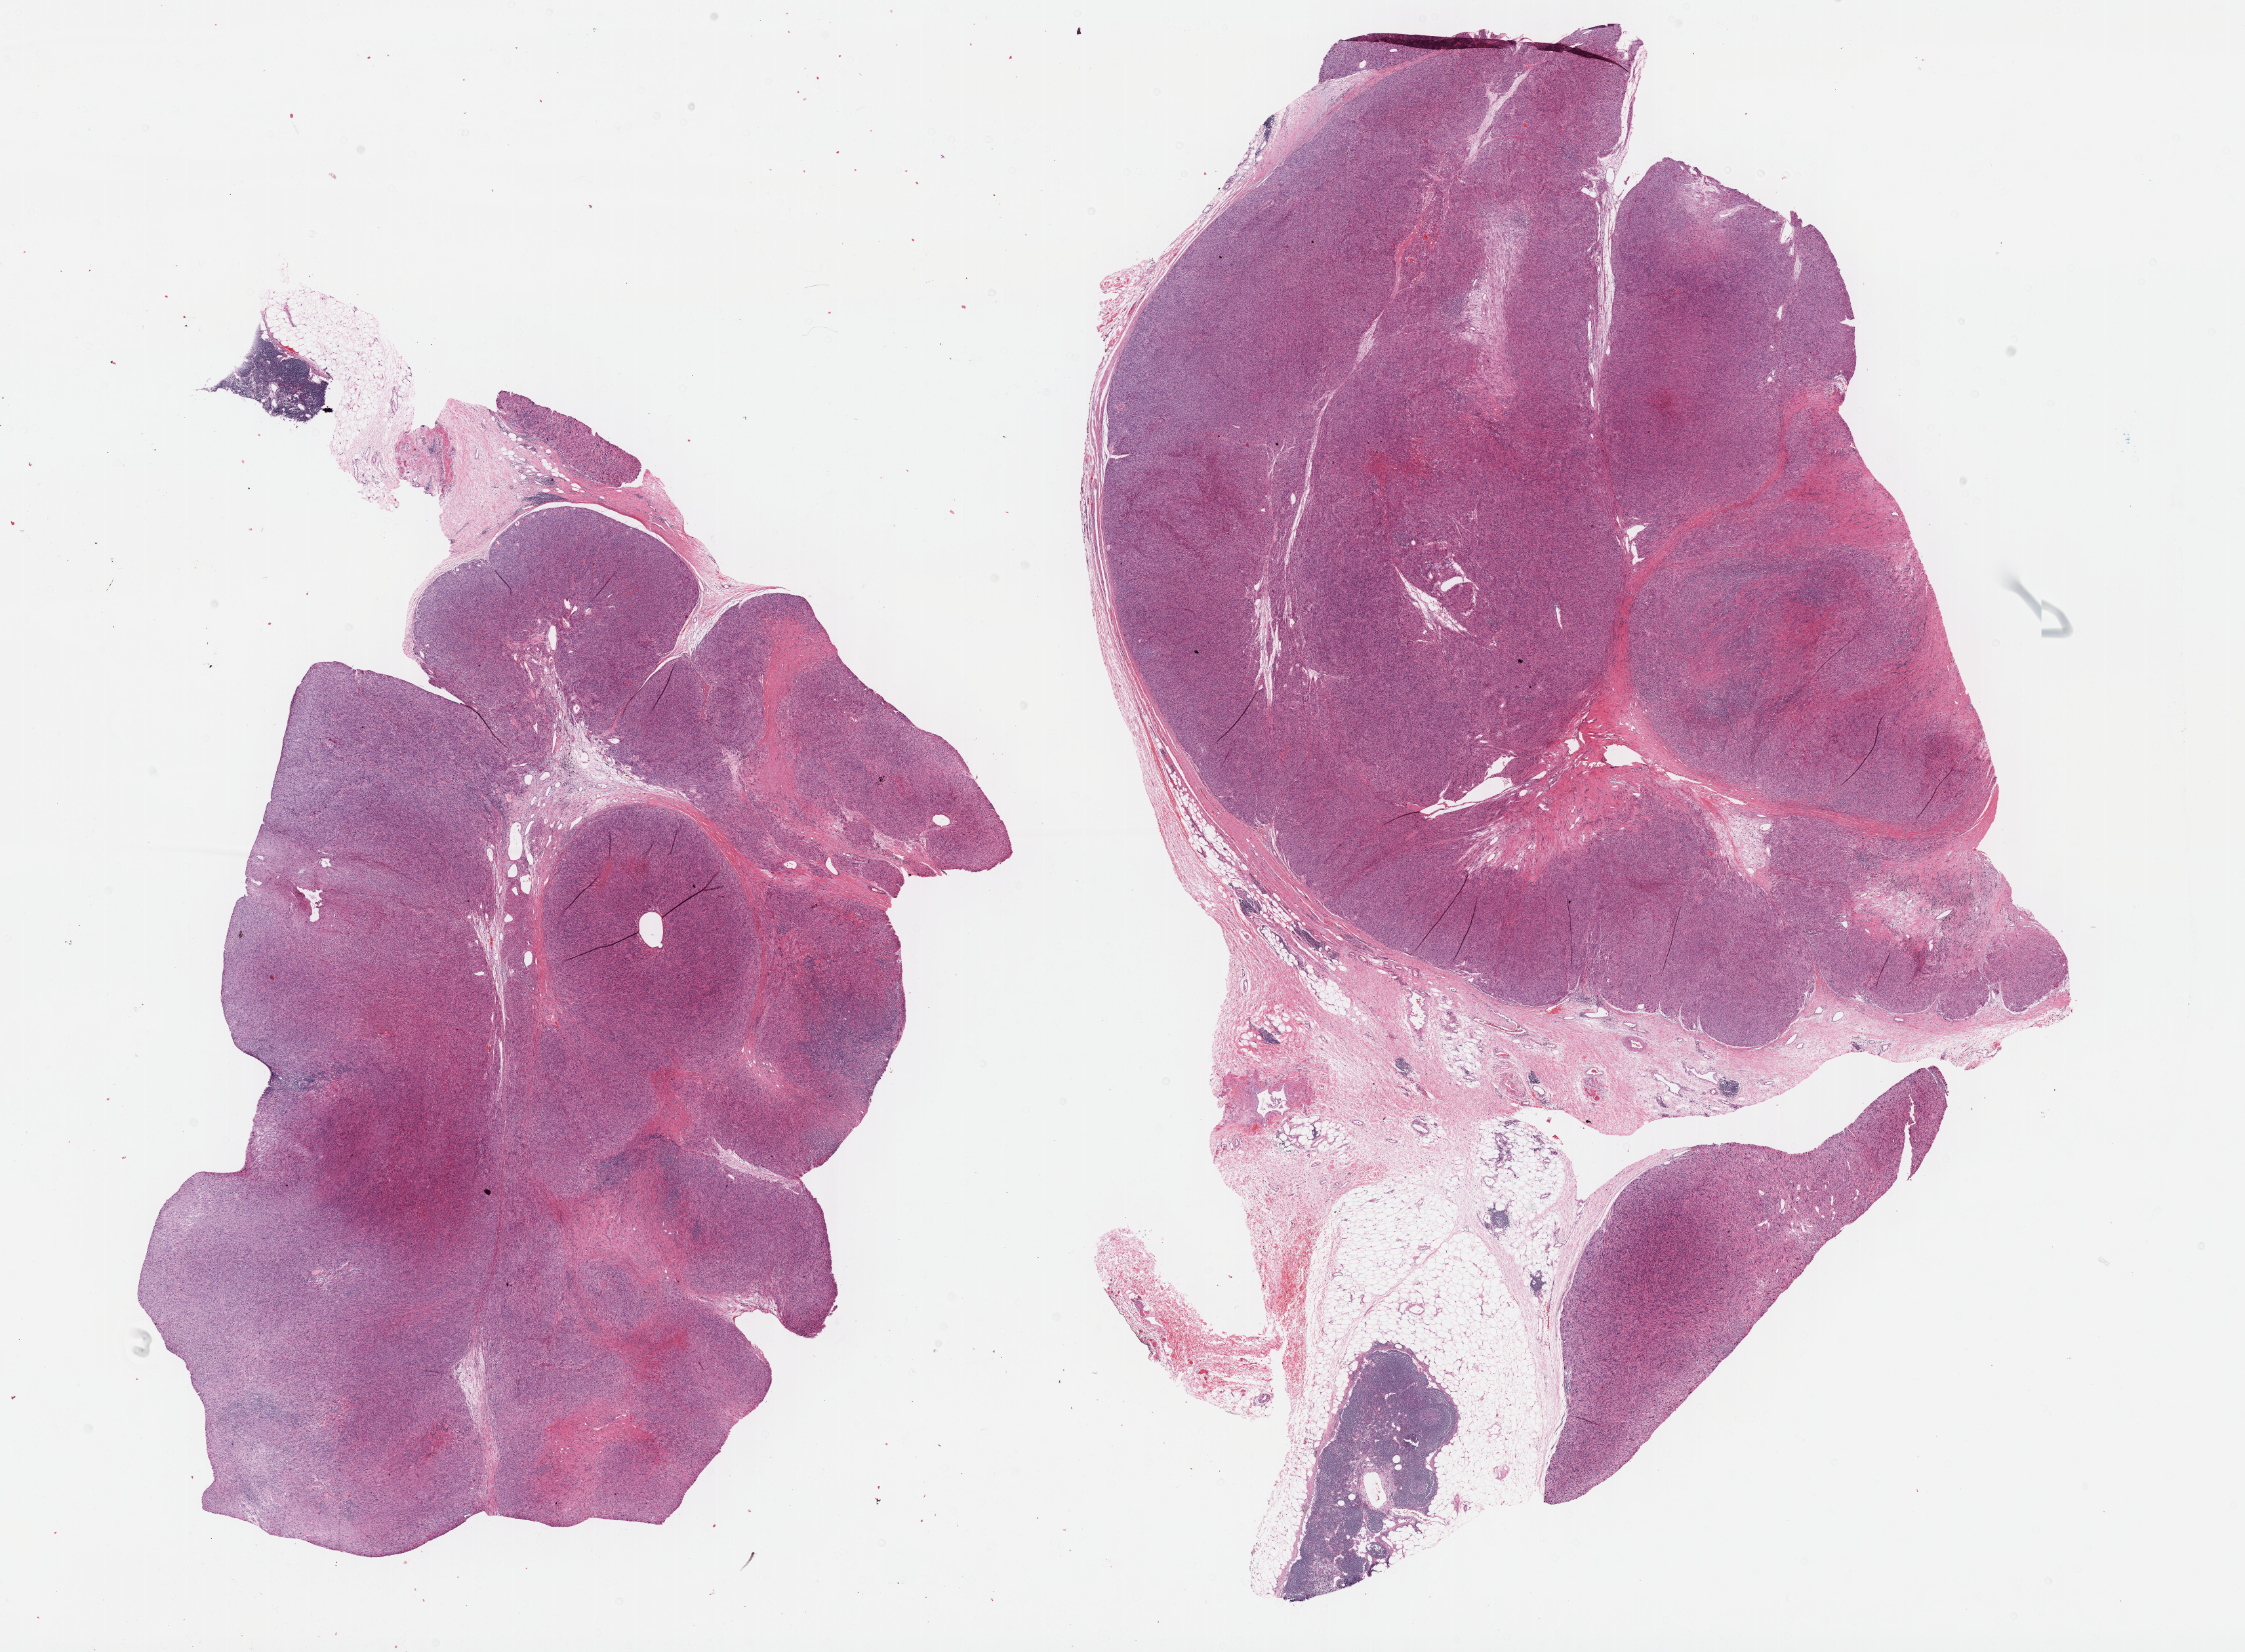
Whole-slide histology image, H&E, shown as a low-resolution overview of the whole scanned area (about 27.7 x 20.4 mm, acquisition: 40x scan). Formalin-fixed paraffin-embedded (FFPE) diagnostic section. Sample: primary tumour, retroperitoneum and peritoneum. Patient: male, age at initial diagnosis 70 years.
Pathologic diagnosis: Leiomyosarcoma, NOS (retroperitoneum).